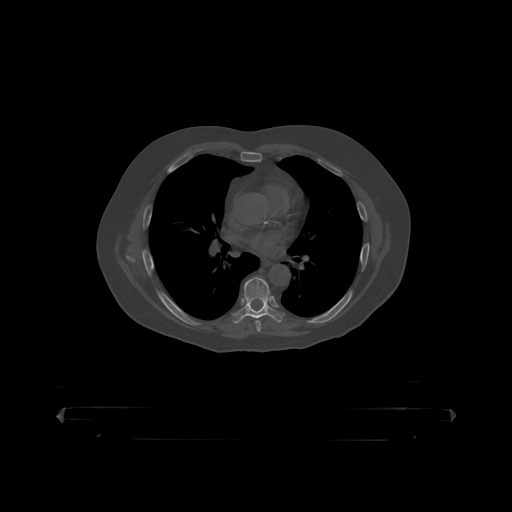
CT including the spine, one axial slice. Position 283 of 390 along the scan axis. 120 kVp. Bone window (W 1800 / L 400 HU). 1.25 mm slice thickness. 512 × 512 image matrix, field of view 650 × 650 mm. Male patient, age 60 years. Case-level facts recorded for this patient, not image findings: primary cancer: prostate.
Structures marked on this image (semi-automatic segmentation, software-assisted and operator-edited):
- T7 vertebra: bounding box (x1, y1, x2, y2) in pixels: (235, 278, 280, 319)